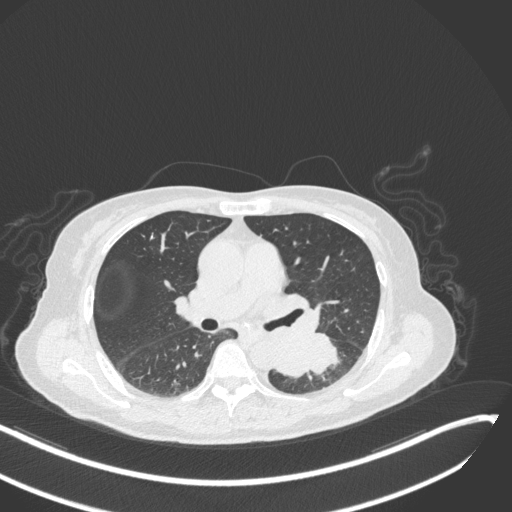
Chest CT, one axial slice. Reconstruction kernel B31f. 120 kVp. Lung window (W 1500 / L -600 HU). 1 mm slice thickness. 512 × 512 image matrix, field of view 400 × 400 mm. Female patient, age 64 years. Case-level facts recorded for this patient, not image findings: clinical TNM (as recorded): T3 N1 M1; histopathological grade: G3.
Annotated regions visible in this slice (bounding box drawn by a radiologist):
- lung tumour (recorded histology: small cell carcinoma): bounding box [x1, y1, x2, y2] px = [276, 331, 344, 385]